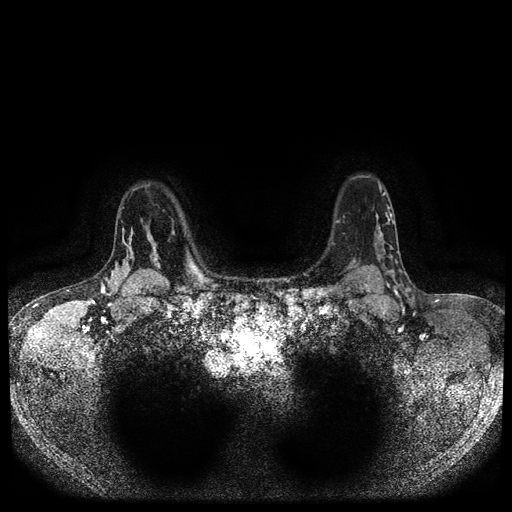
Breast MRI (dynamic contrast-enhanced, multi-phase), one axial slice. Position 78 of 116 along the scan axis. Dynamic contrast-enhanced series, time point 2 of 5 at this slice position (early post-contrast). 1.5 T. TE 2.6 ms, TR 5.4 ms. 512 × 512 image matrix, field of view 340 × 340 mm. Female patient, age 47 years.
Outlined on this slice (semi-automatic segmentation, software-assisted and operator-edited):
- breast lesion (labelled 'tumour' in the annotation; benign lesions carry a separate 'benign' label): bounding box (x1, y1, x2, y2) in pixels: (146, 234, 163, 274)